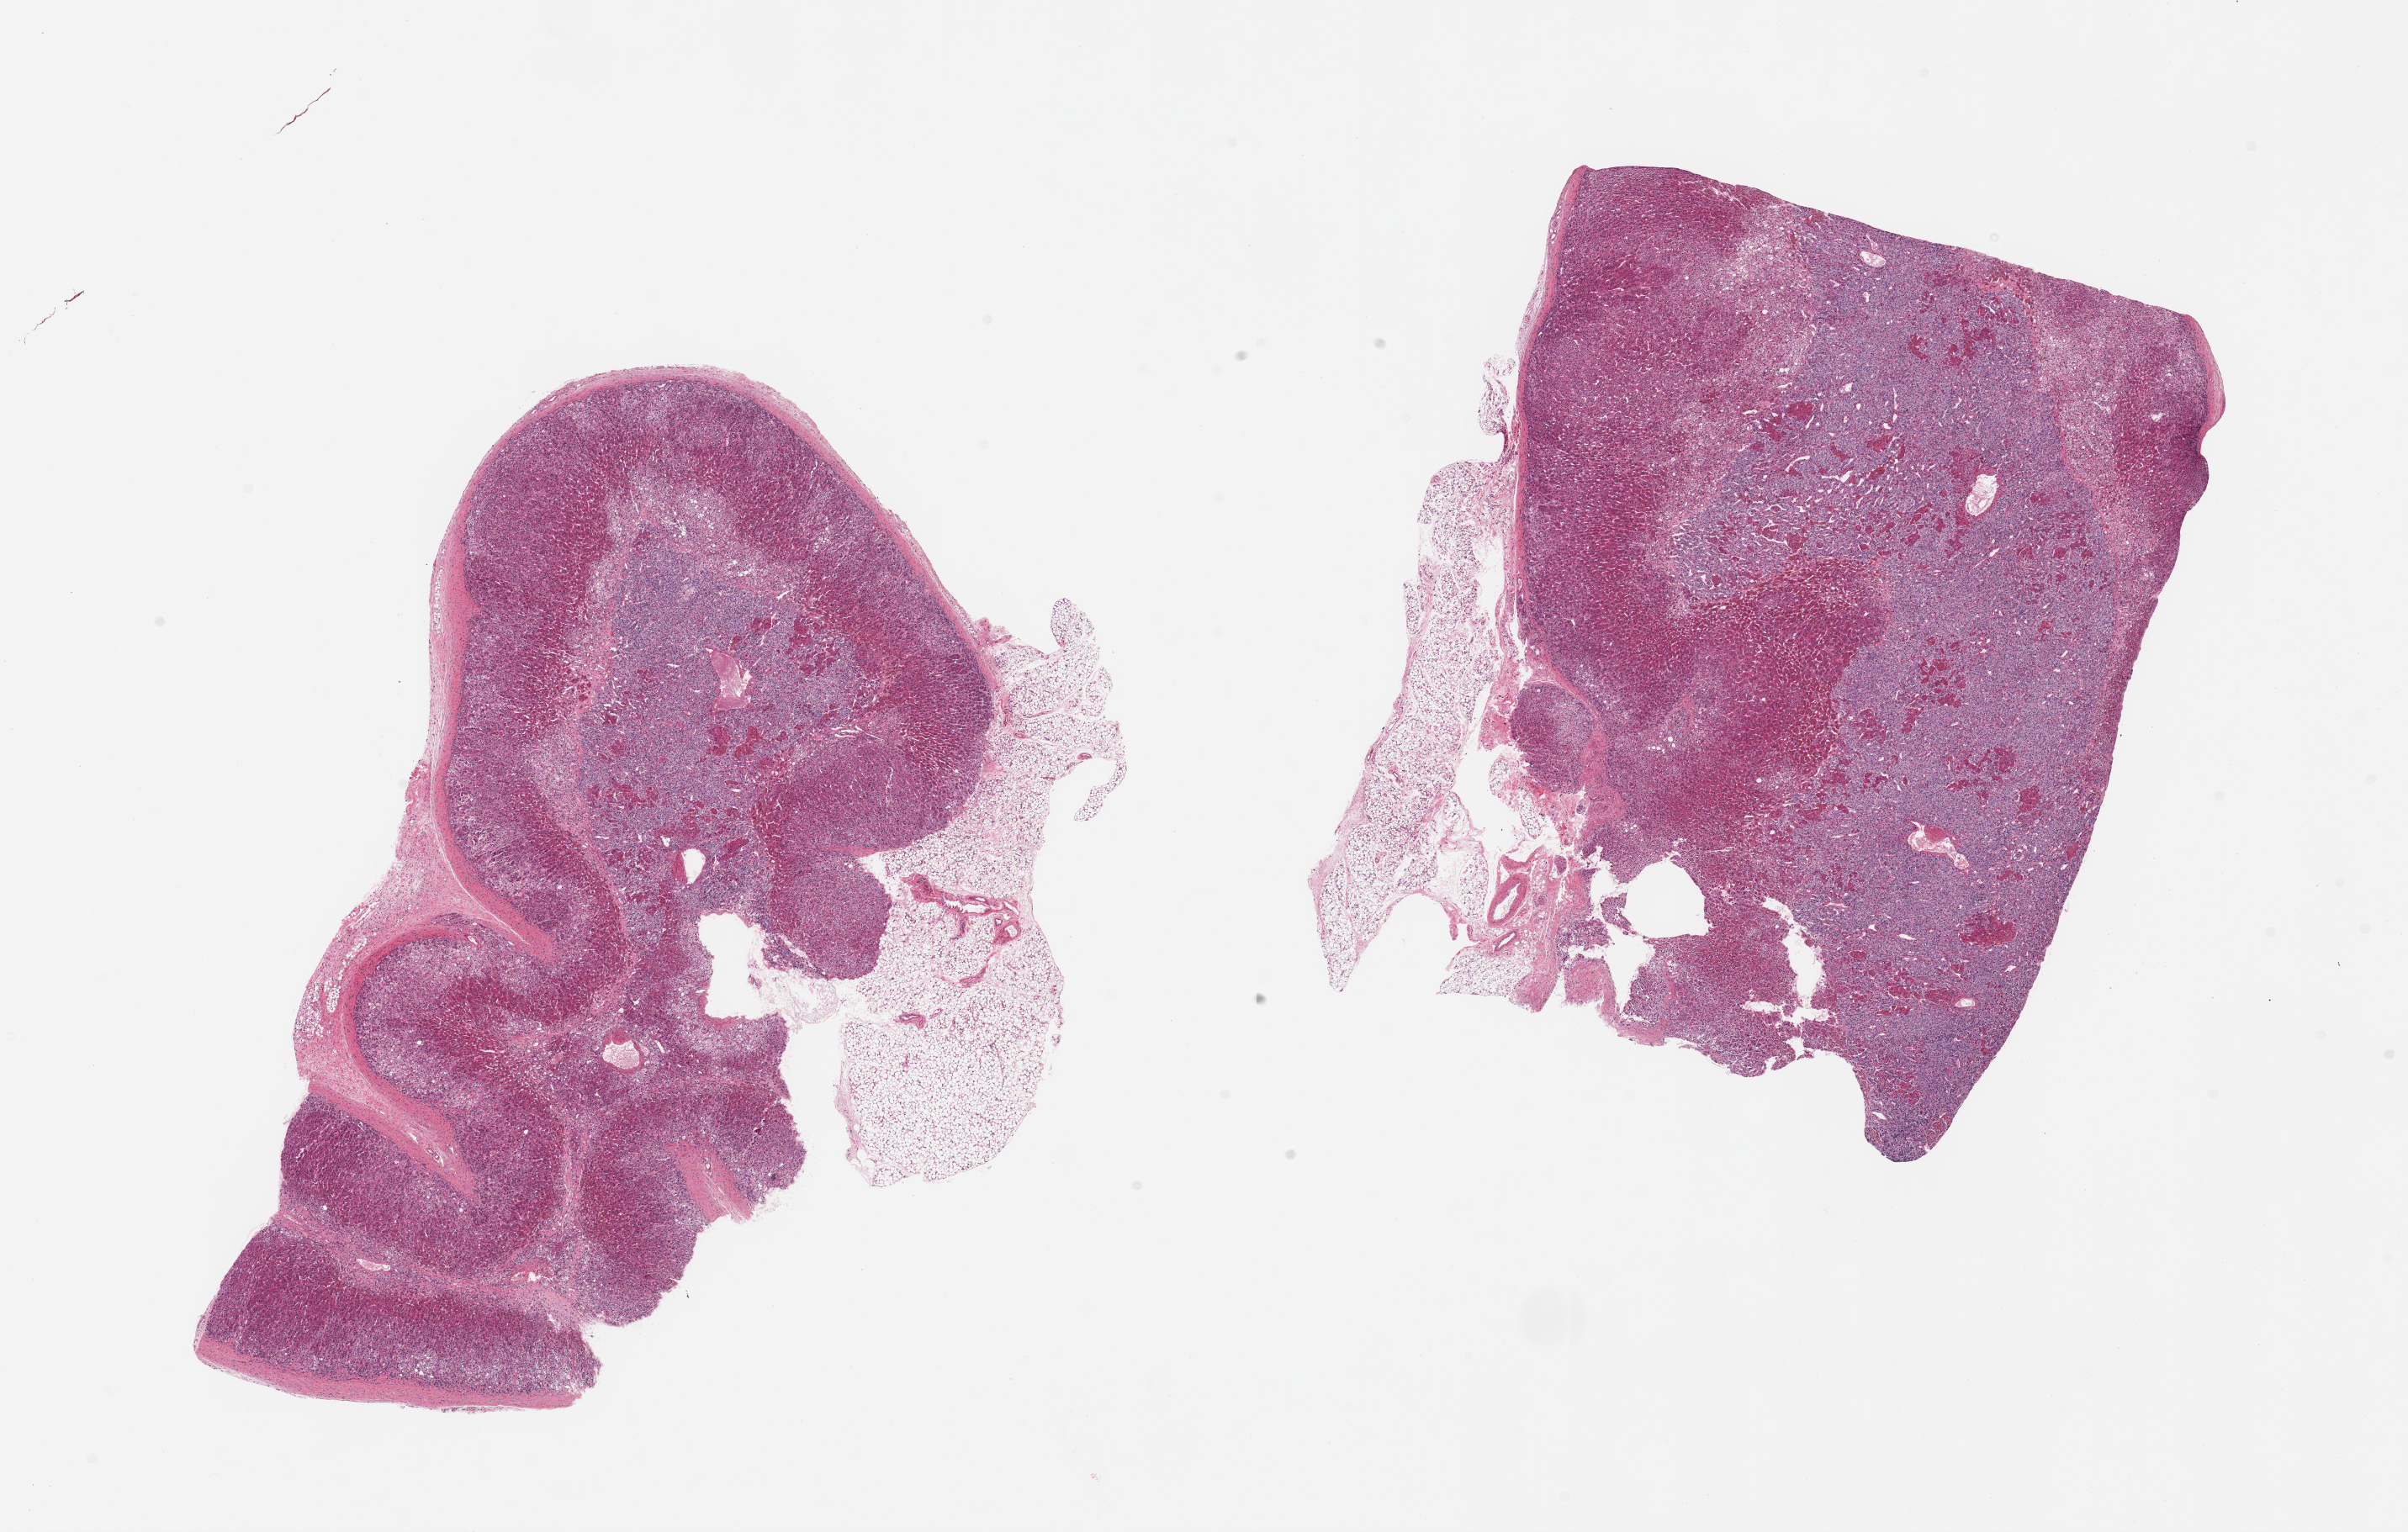
Digitized hematoxylin and eosin (H&E)-stained section — shown as a low-resolution overview of the whole scanned area (about 22.6 x 14.4 mm, from a 20x scan). PAXgene-fixed paraffin-embedded (PFPE) section. Sampled site (target tissue): adrenal gland. Donor tissue sample.
Pathologist's review note for this sample: 2 pieces, prominent medulla, well preserved--valuable and rare specimen; ~10% adherent fat, rep.